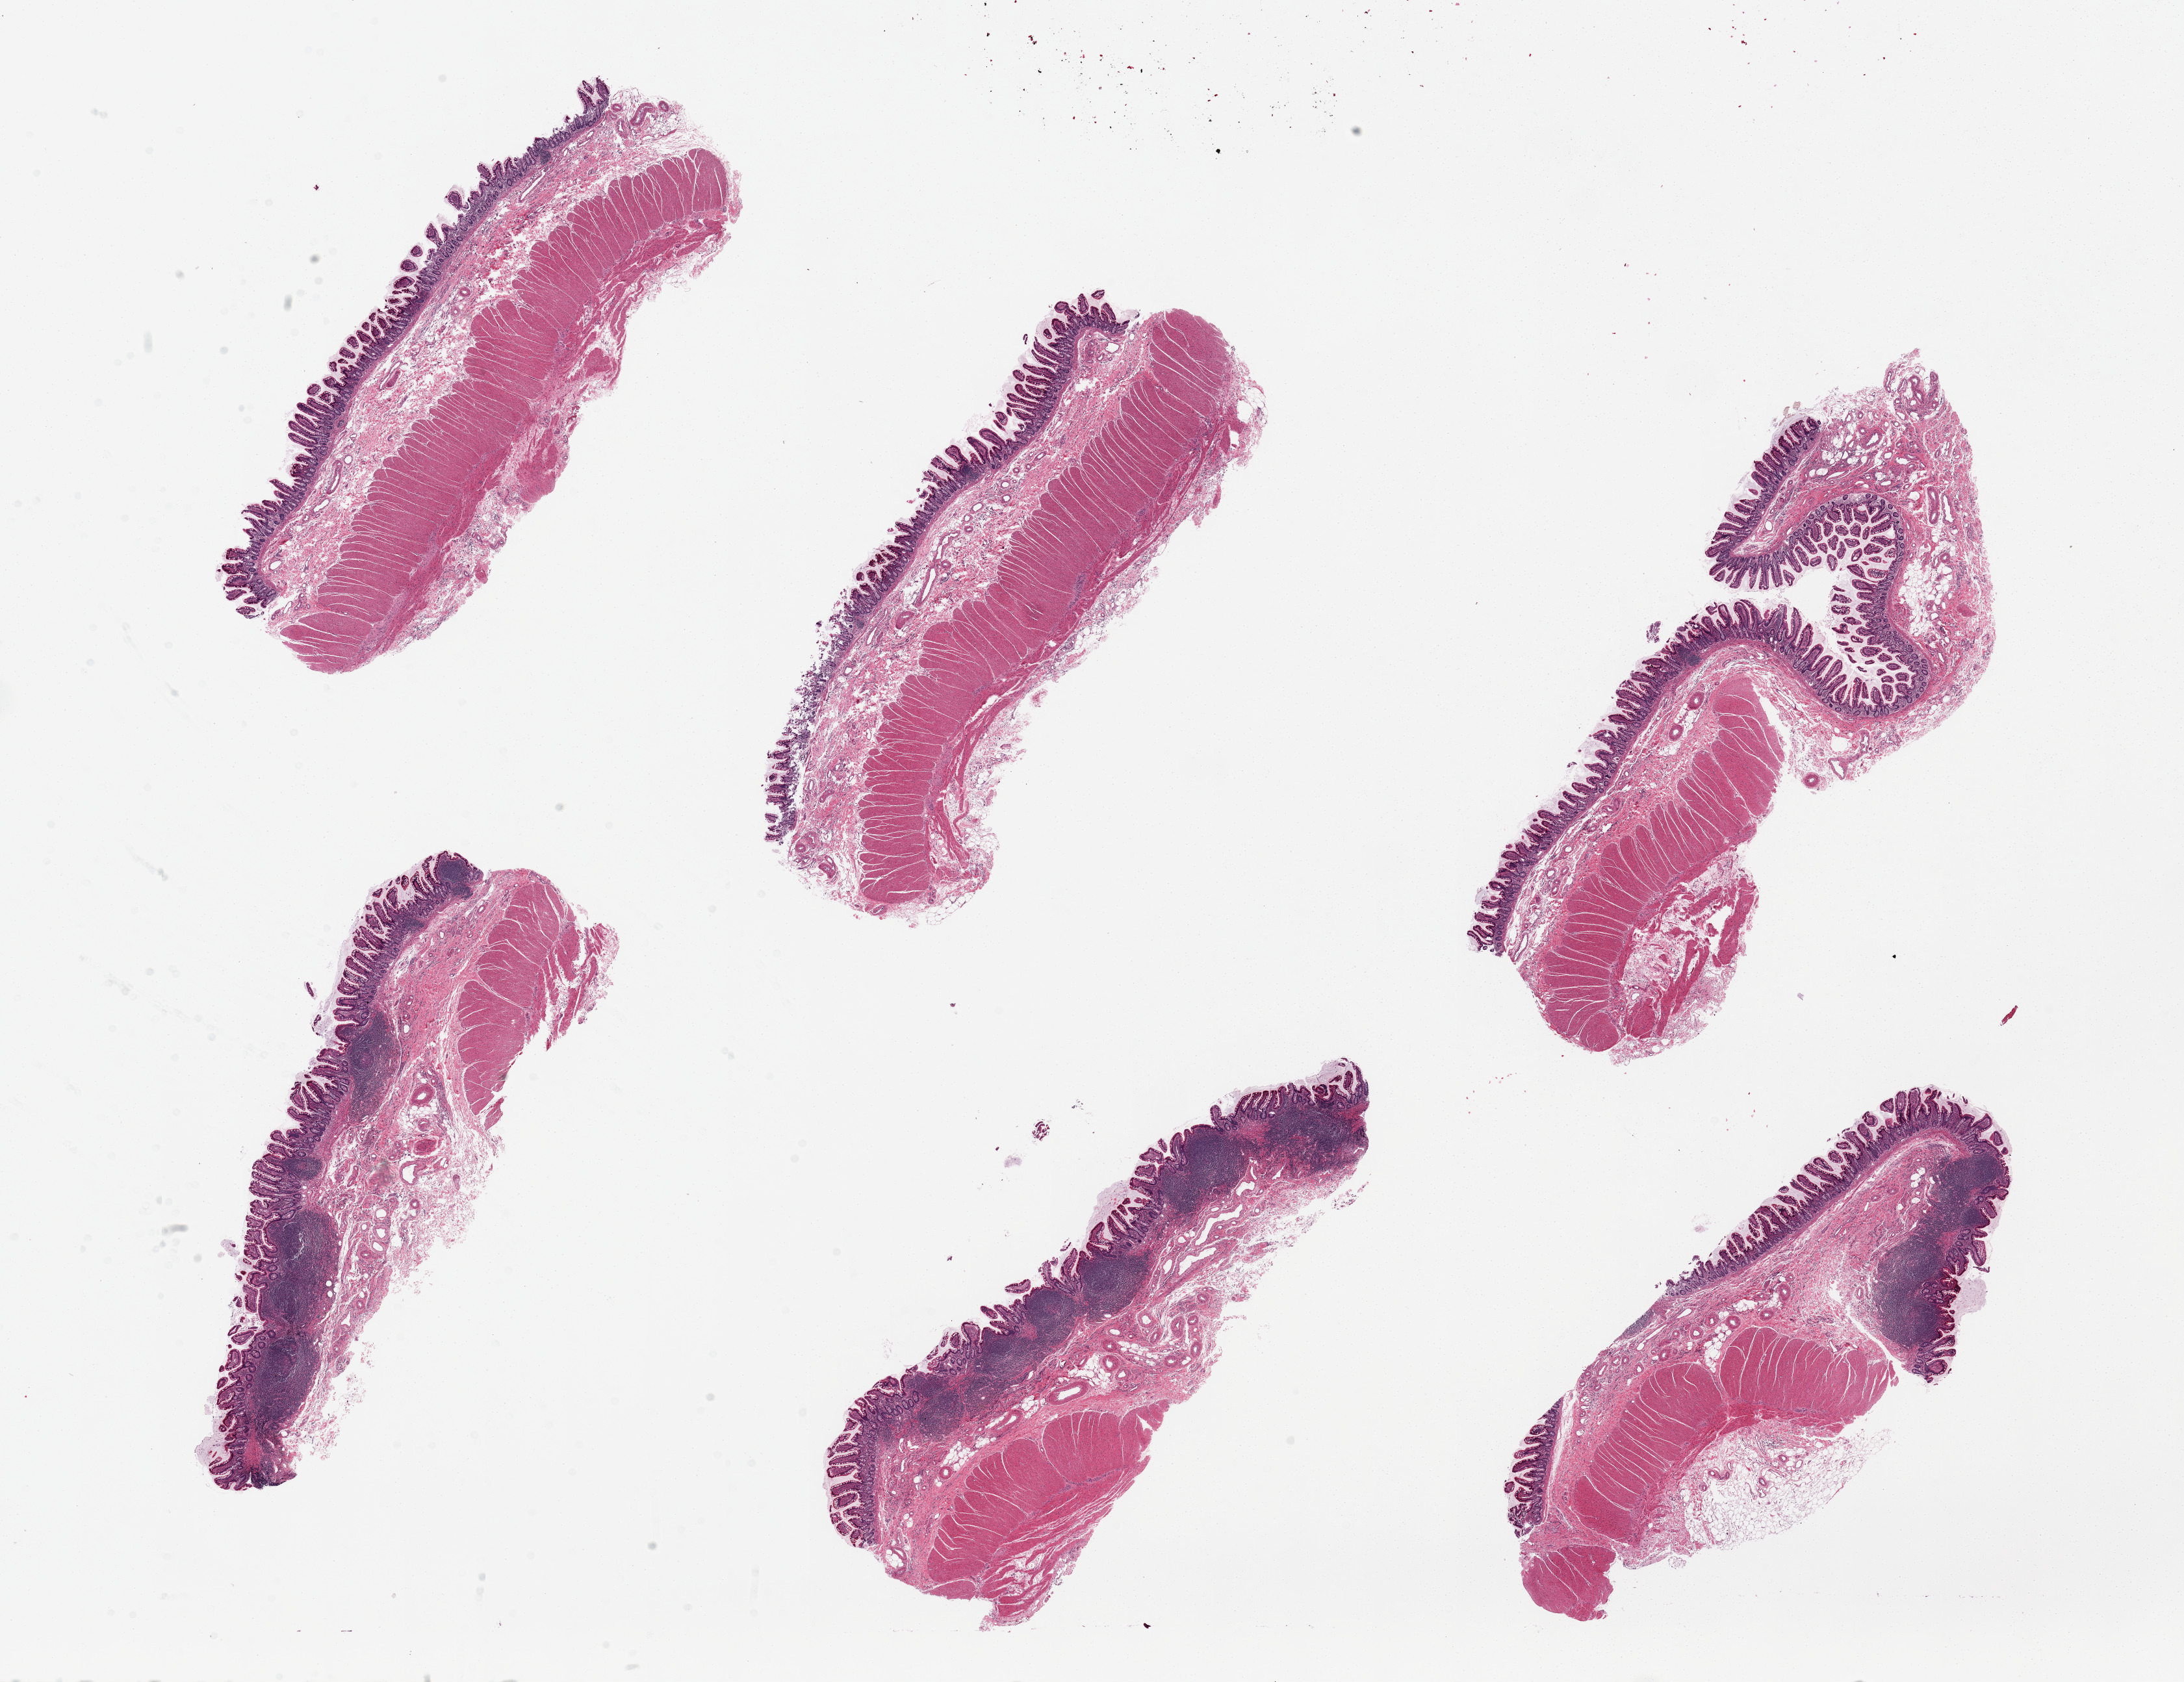
Hematoxylin and eosin (H&E) whole-slide image, whole scanned area (about 26.6 x 20.5 mm) shown as a low-resolution overview; PAXgene-fixed, paraffin-embedded tissue; section of ileum (target tissue); tissue donor sample. Donor sex: male.
Pathologist's review note for this sample: 6 pieces; muscularis propria present in several pieces (not target); lymphoid elements prominent in several pieces.